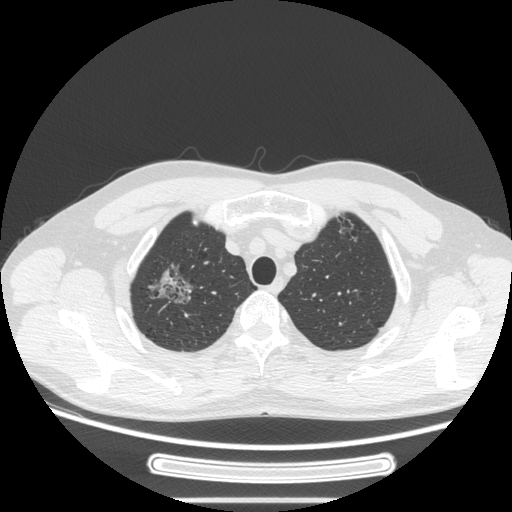
Chest CT, one axial slice; slice 223 of 269 in the series (ordered by position); reconstruction kernel STANDARD; 120 kVp; lung window (W 1500 / L -600 HU); 512 × 512 image matrix, field of view 382 × 382 mm. Patient: male, 53 years. Case-level facts recorded for this patient, not image findings: clinical TNM (as recorded): T1c N0 M0; histopathological grade: G2.
Outlined on this slice (bounding box drawn by a radiologist):
- lung tumour (recorded histology: adenocarcinoma): bounding box (x1, y1, x2, y2) in pixels: (147, 261, 196, 312)